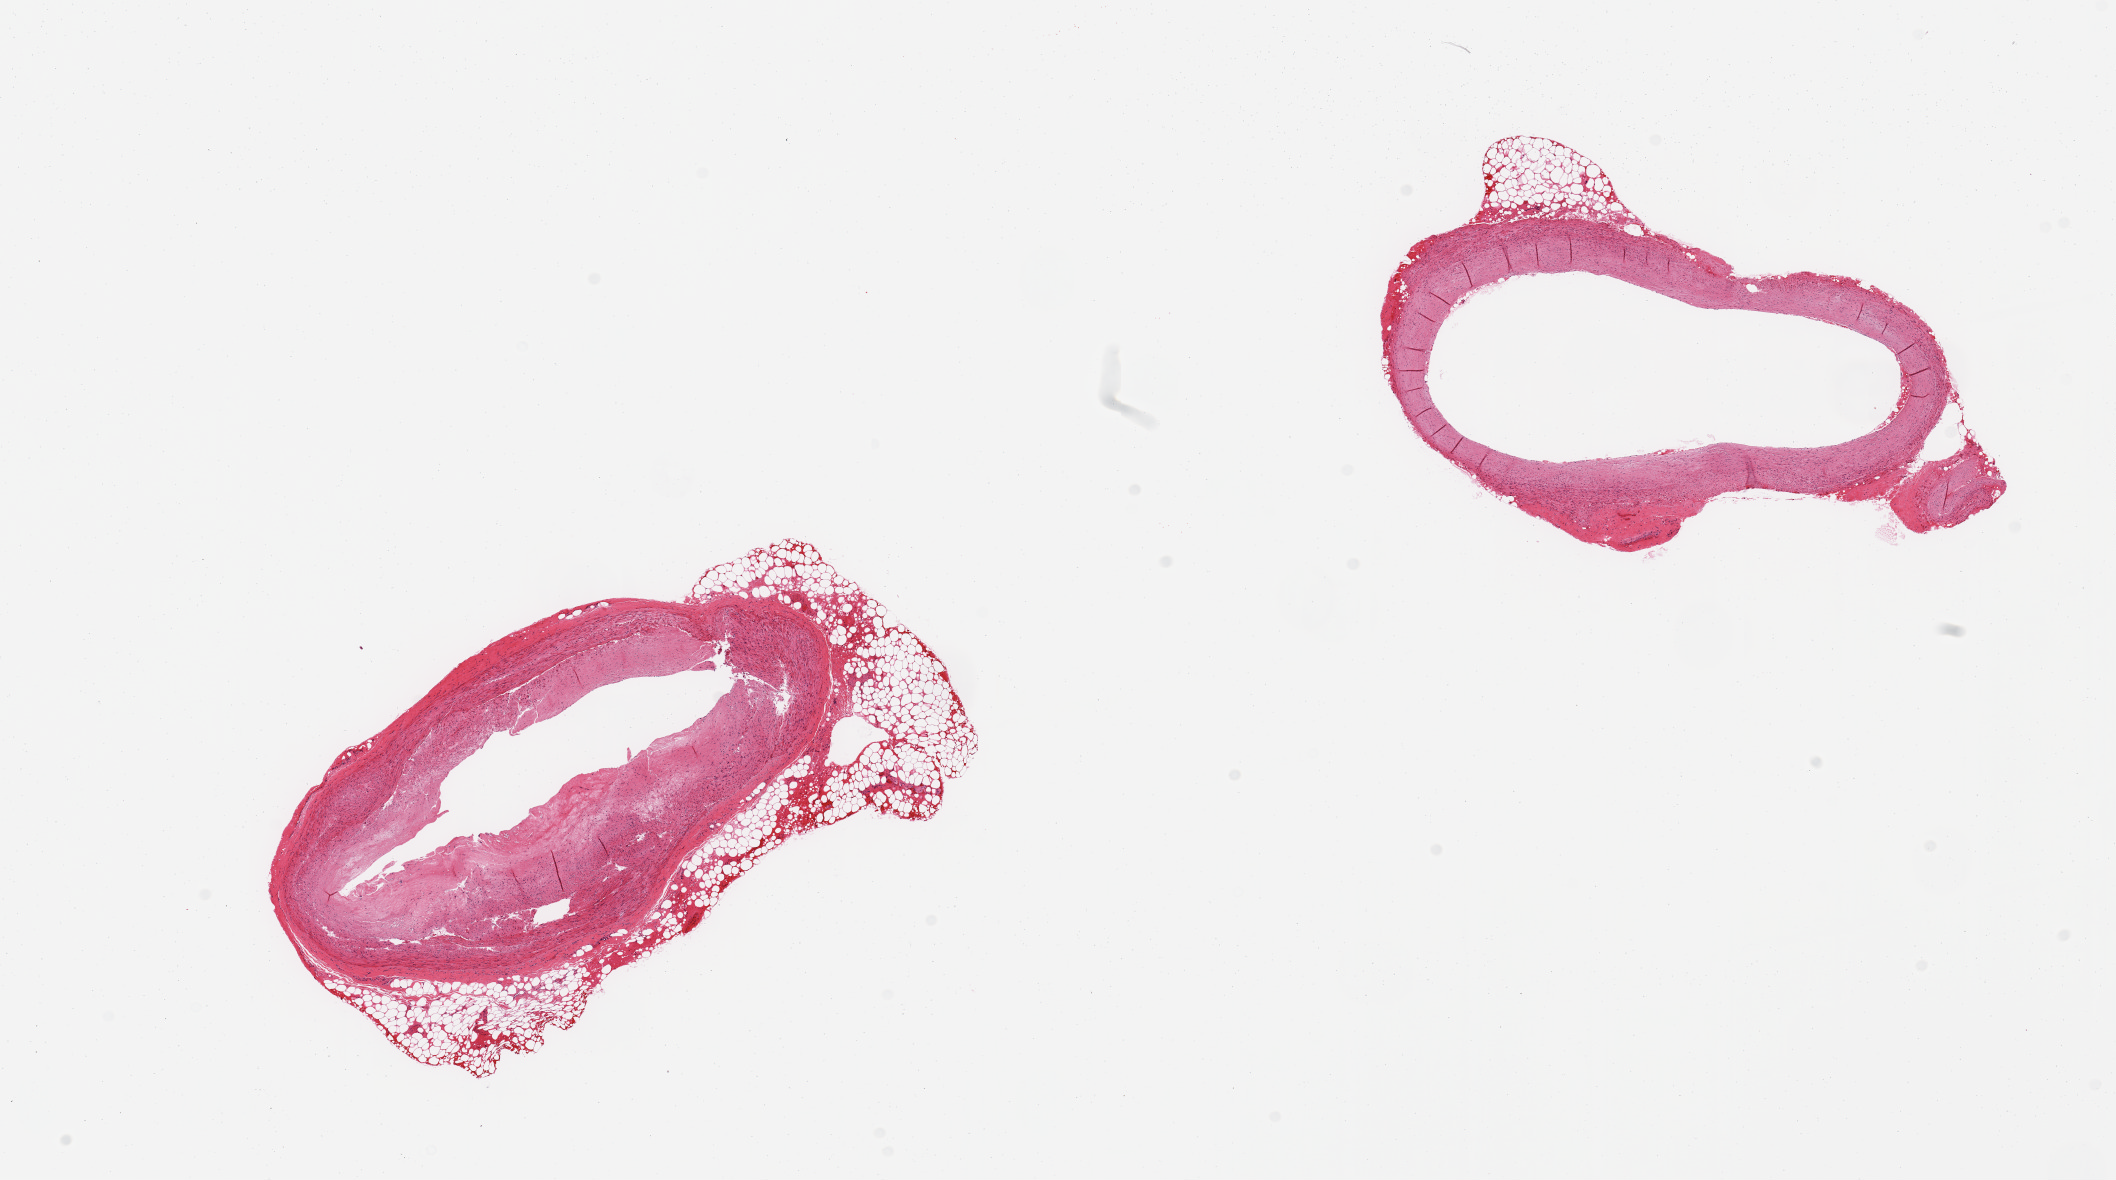
Haematoxylin and eosin whole-slide image, brightfield — a low-resolution overview of the entire scanned area, about 16.7 x 9.3 mm (from a 20x scan); PAXgene-fixed paraffin-embedded (PFPE) section; section of coronary artery (target tissue); donor tissue sample.
- reviewer comment on this tissue sample: 2 pieces; adherent partial rim of fat, ~1mm; subtotally occlusive atherosis (~80%) in one section